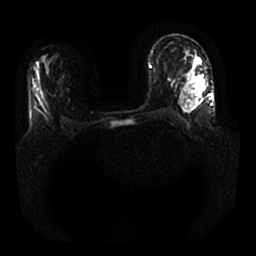
Breast MRI, one axial slice; position 13 of 25 along the scan axis; diffusion-weighted series; image 2 of 4 stored at this slice position (different b-values; order by instance number); 1.5 T; 4 mm slice thickness; 256 × 256 image matrix, field of view 340 × 340 mm. Female patient.
Annotated regions visible in this slice (manually delineated by an expert):
- tumour on diffusion-weighted imaging: bounding box <192,76,205,86> (left, top, right, bottom; pixels)